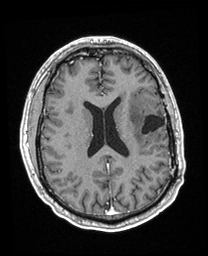
Brain MRI from a brain-tumour surgery series, one axial slice; position 91 of 208 along the scan axis; T1-weighted post-contrast; 1 mm slice thickness; 208 × 256 image matrix, field of view 211 × 260 mm. From the clinical record (not read from this slice): histopathology: Astrocytoma; WHO grade: 3; IDH mutation: yes; tumour location: Left Insular.
Annotated regions visible in this slice (outlined manually by an expert reader):
- previous resection cavity: bounding box <142,115,165,134> (left, top, right, bottom; pixels)